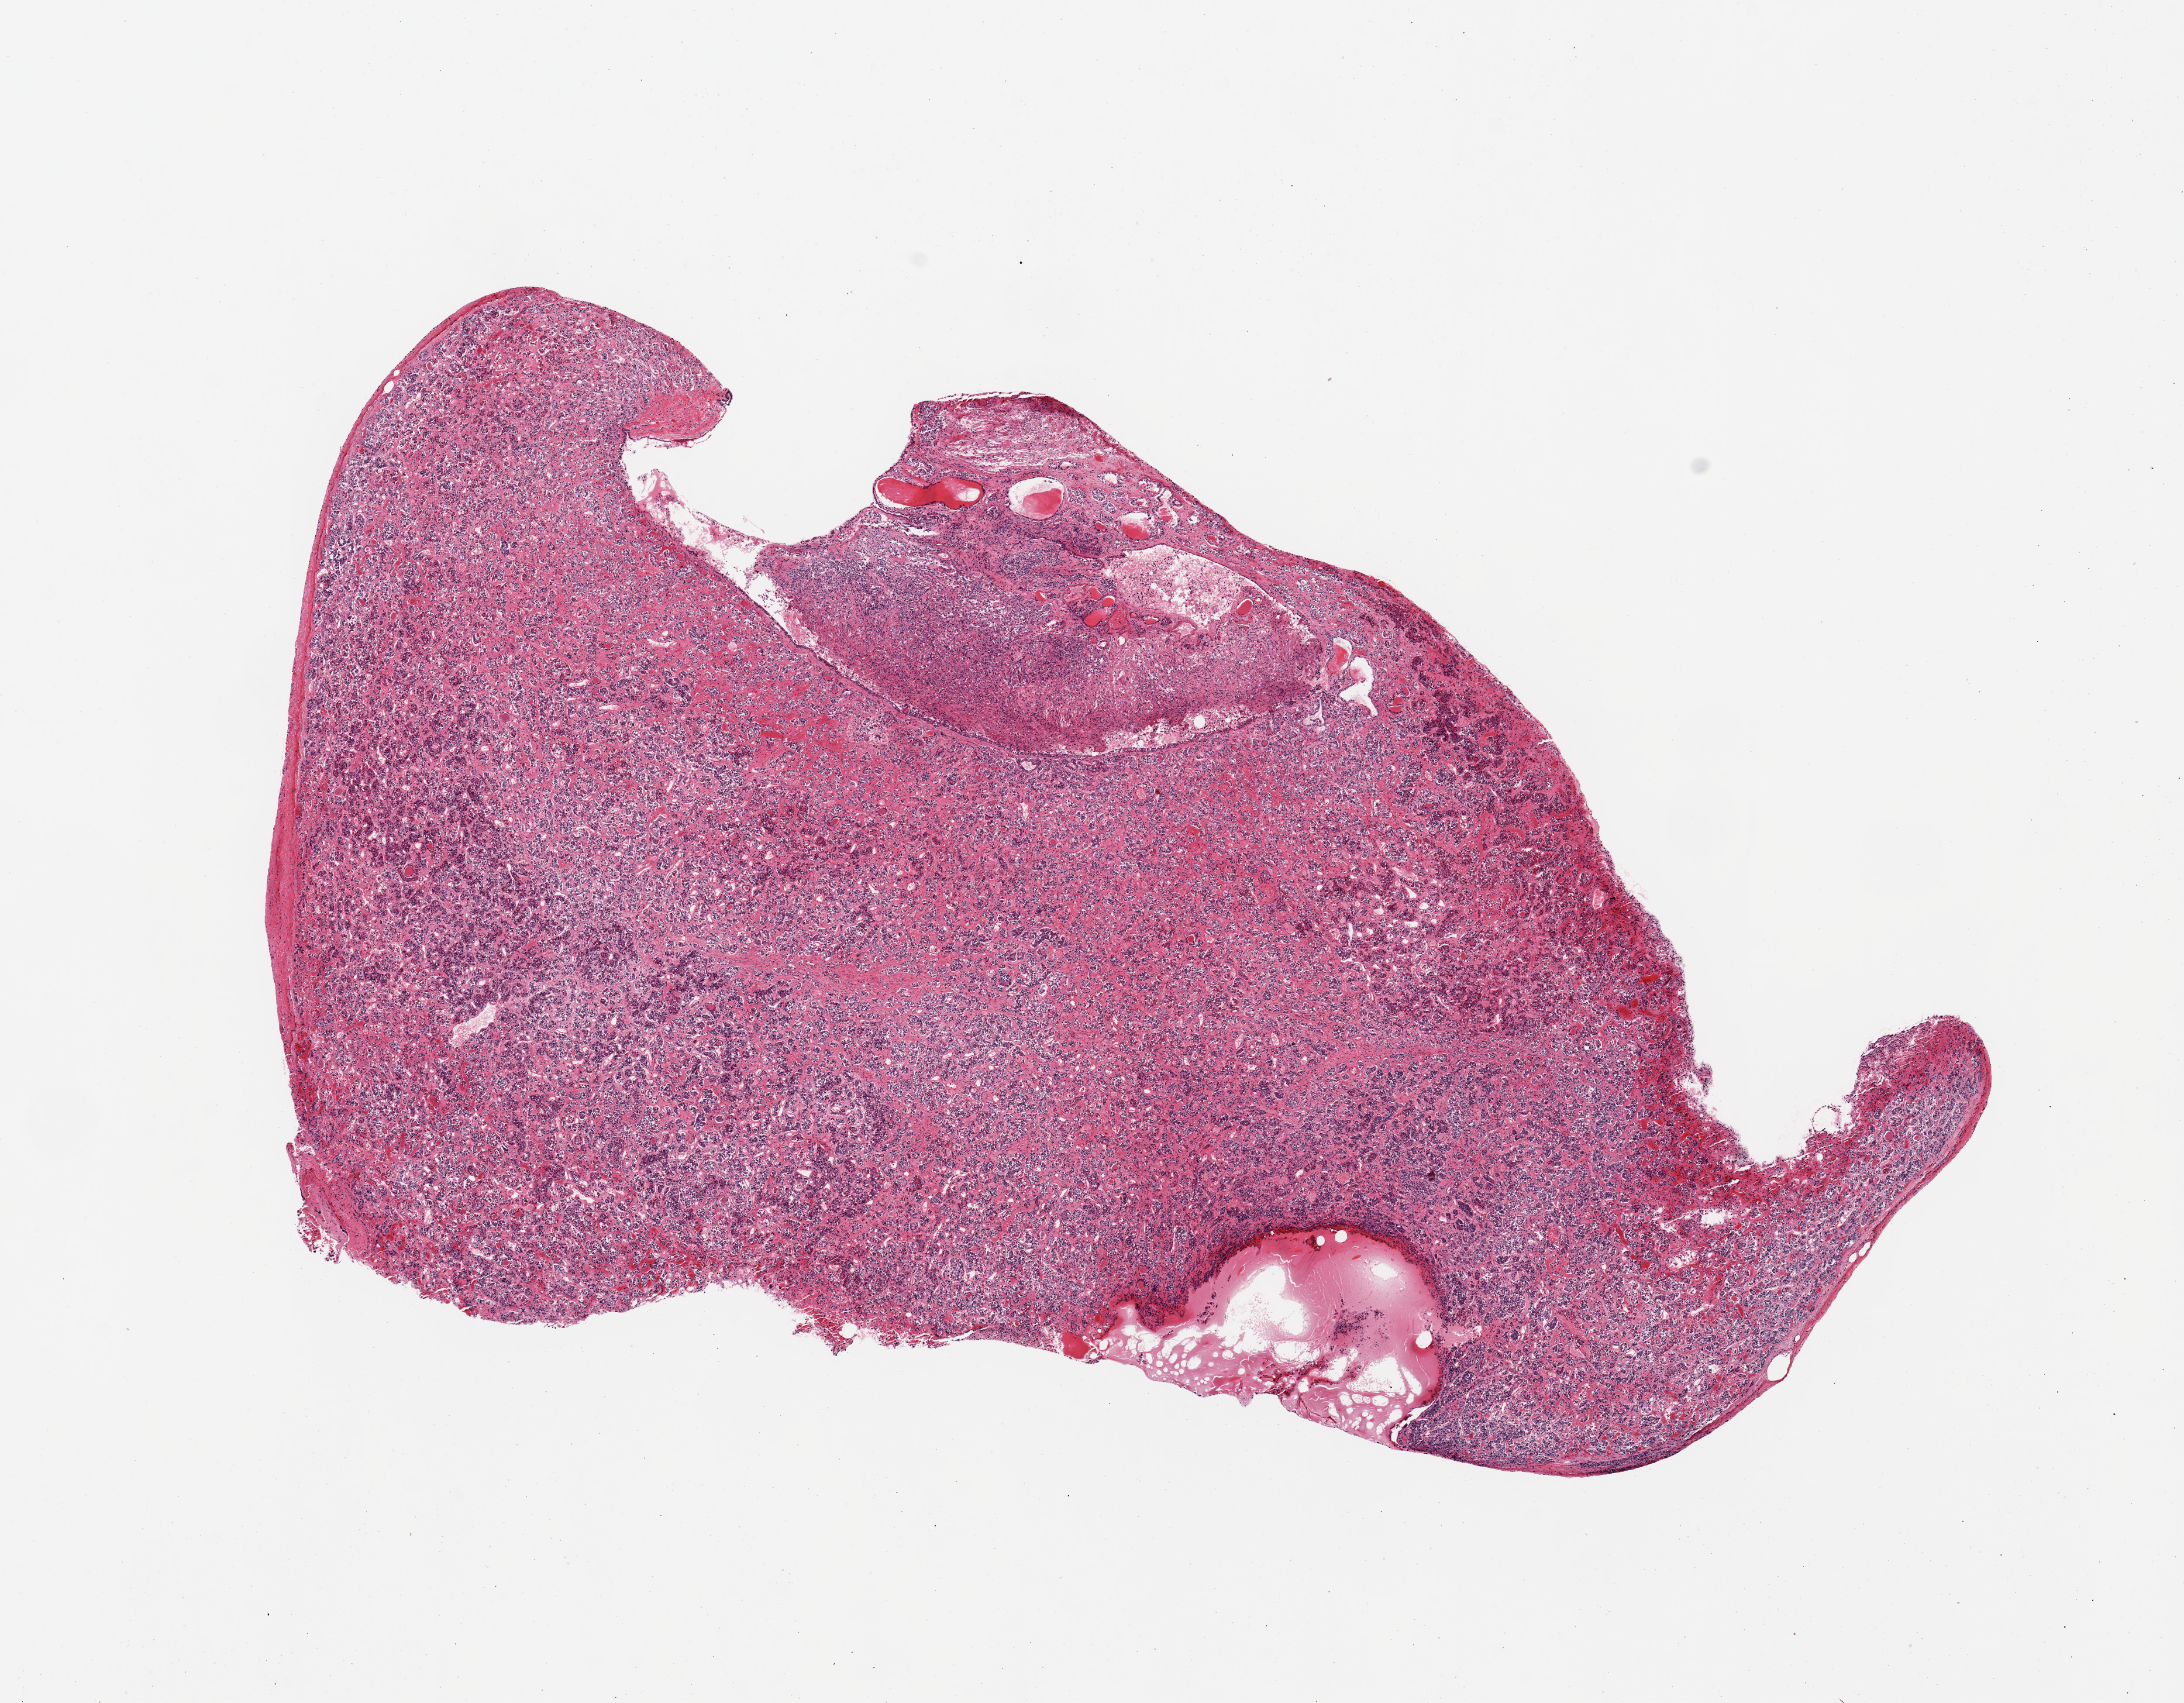
Haematoxylin and eosin whole-slide image — shown as a low-resolution overview of the whole scanned area (about 14.8 x 11.5 mm, slide scanned at 20x). PAXgene-fixed paraffin-embedded (PFPE) section. Section of pituitary (target tissue). Donor tissue sample. Male donor.
* pathologist's review note for this sample: 1 piece; anterior